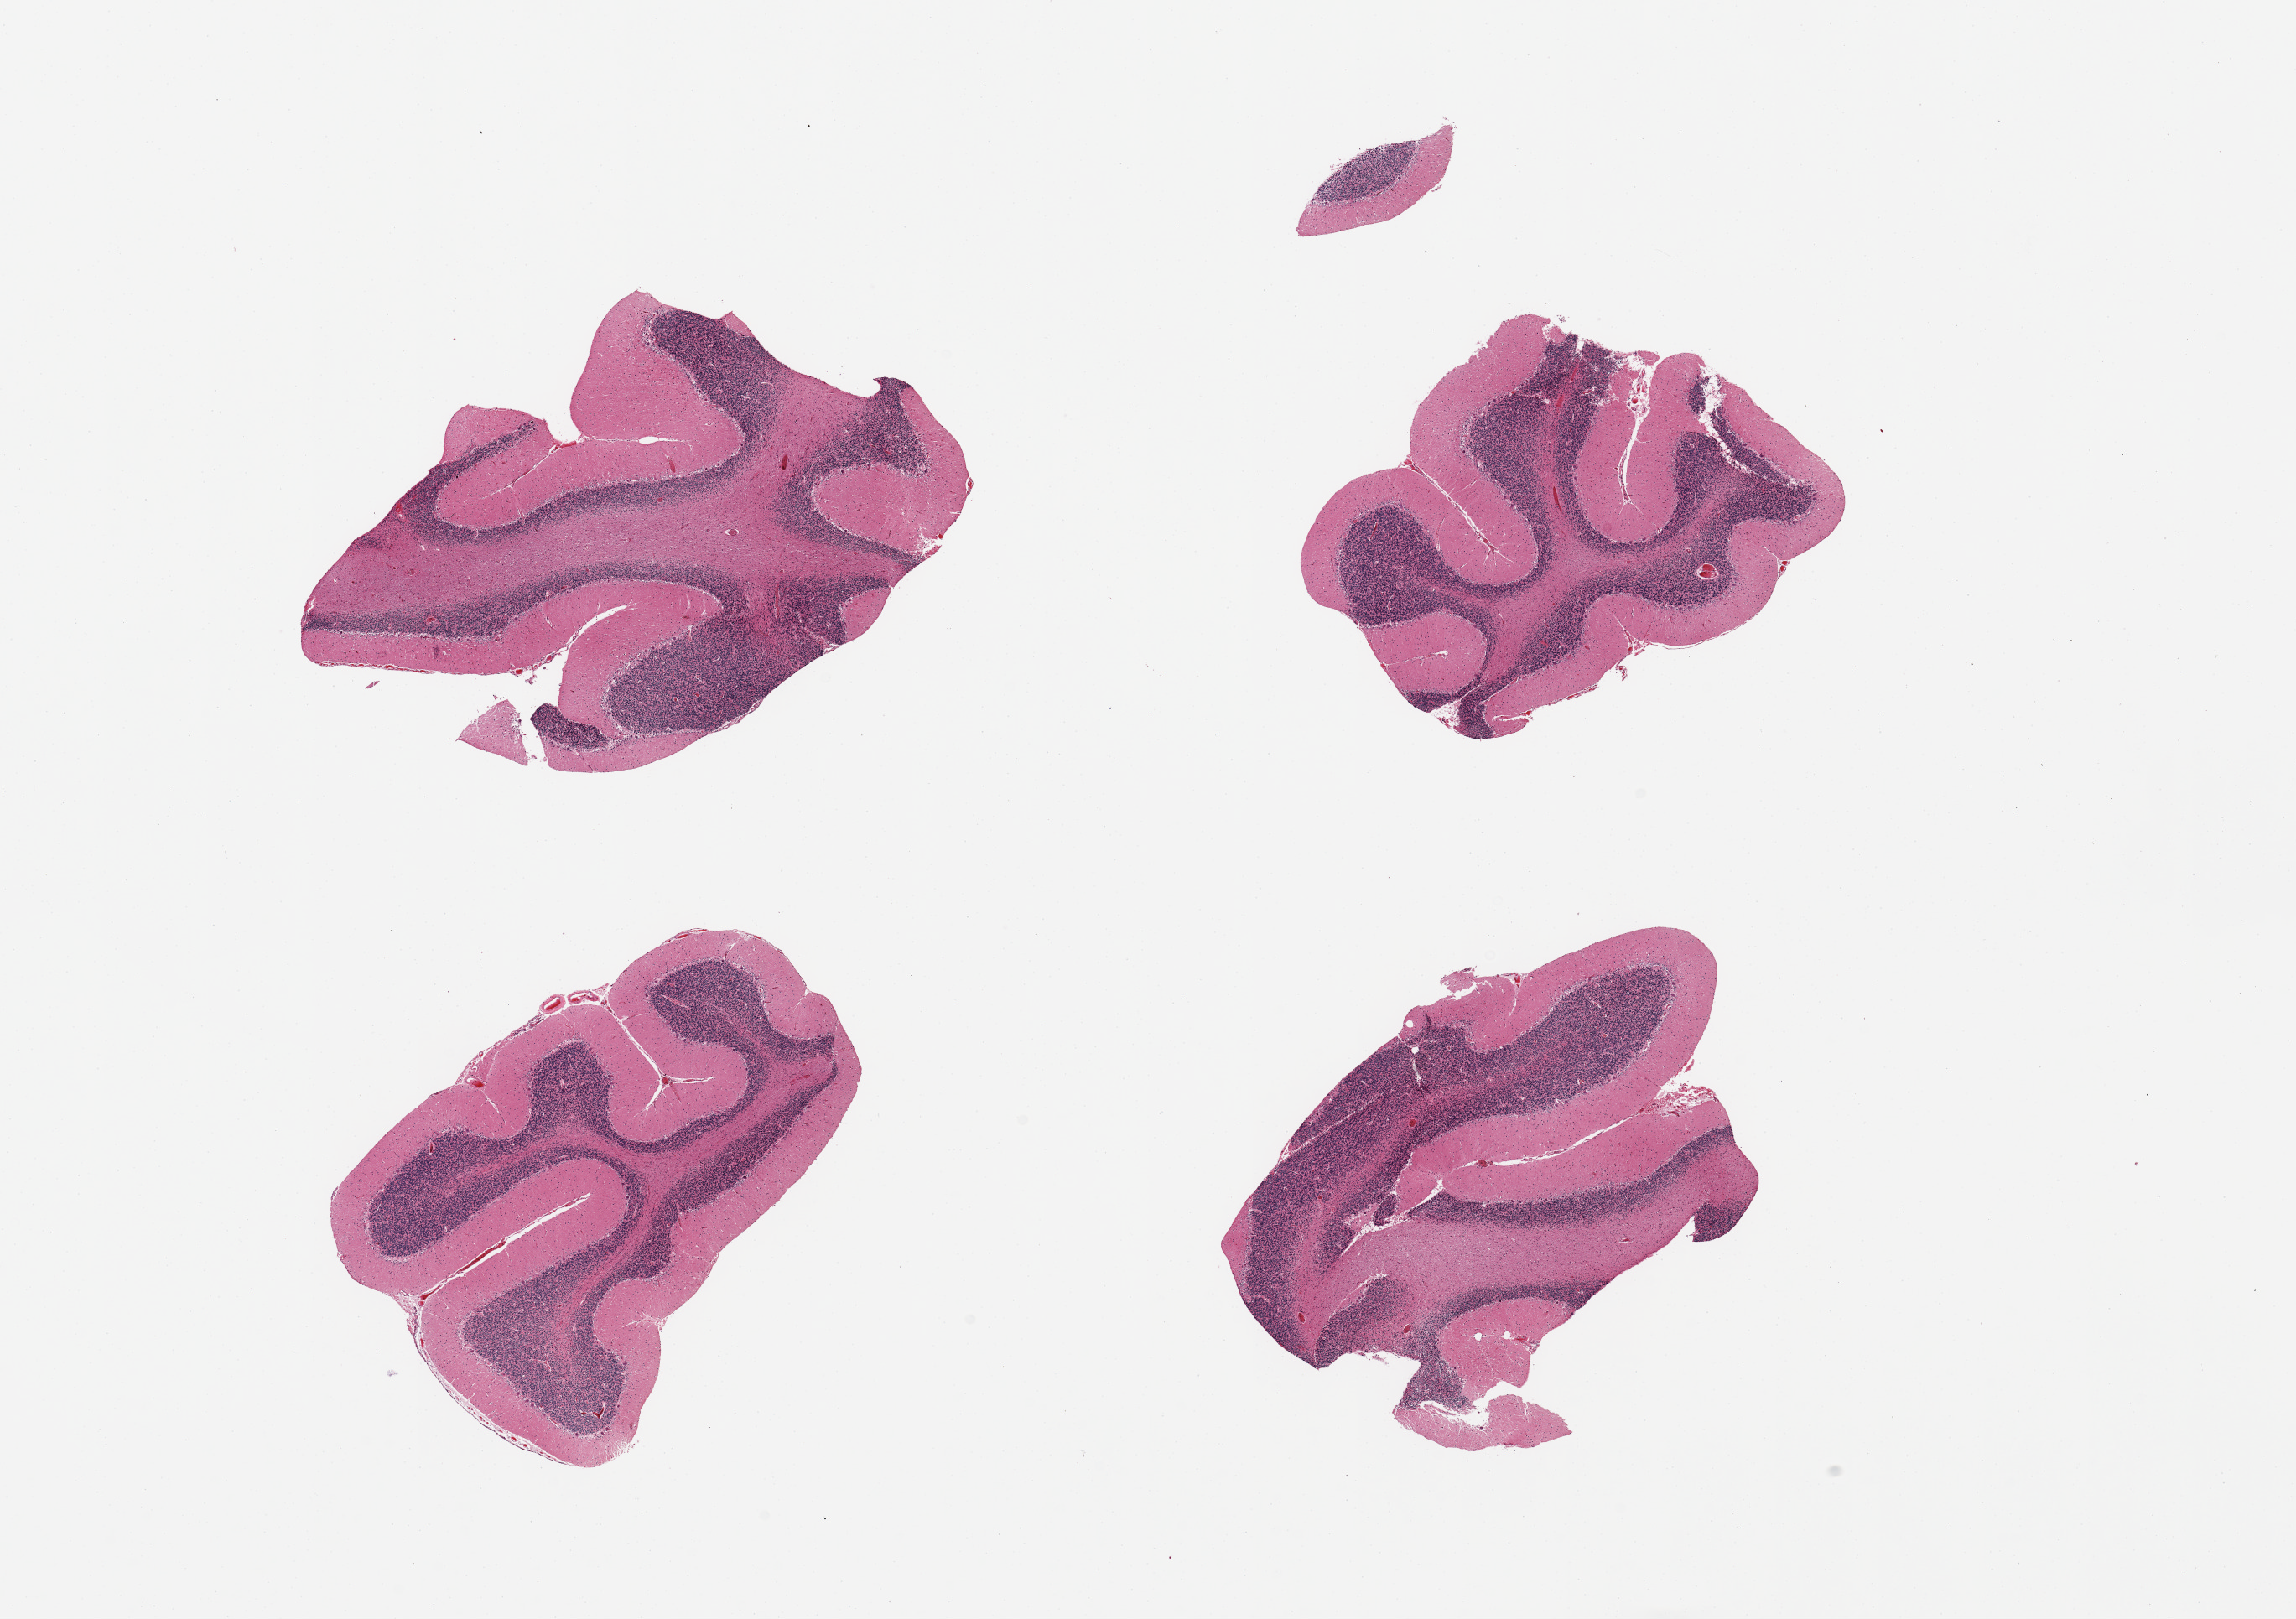
Haematoxylin and eosin whole-slide image, brightfield, a low-resolution overview of the entire scanned area, about 21.7 x 15.3 mm, PAXgene-fixed paraffin-embedded (PFPE) section, sampled site (target tissue): cerebellum, donor tissue sample. Donor sex: female.
- reviewer comment on this tissue sample: 4 pieces